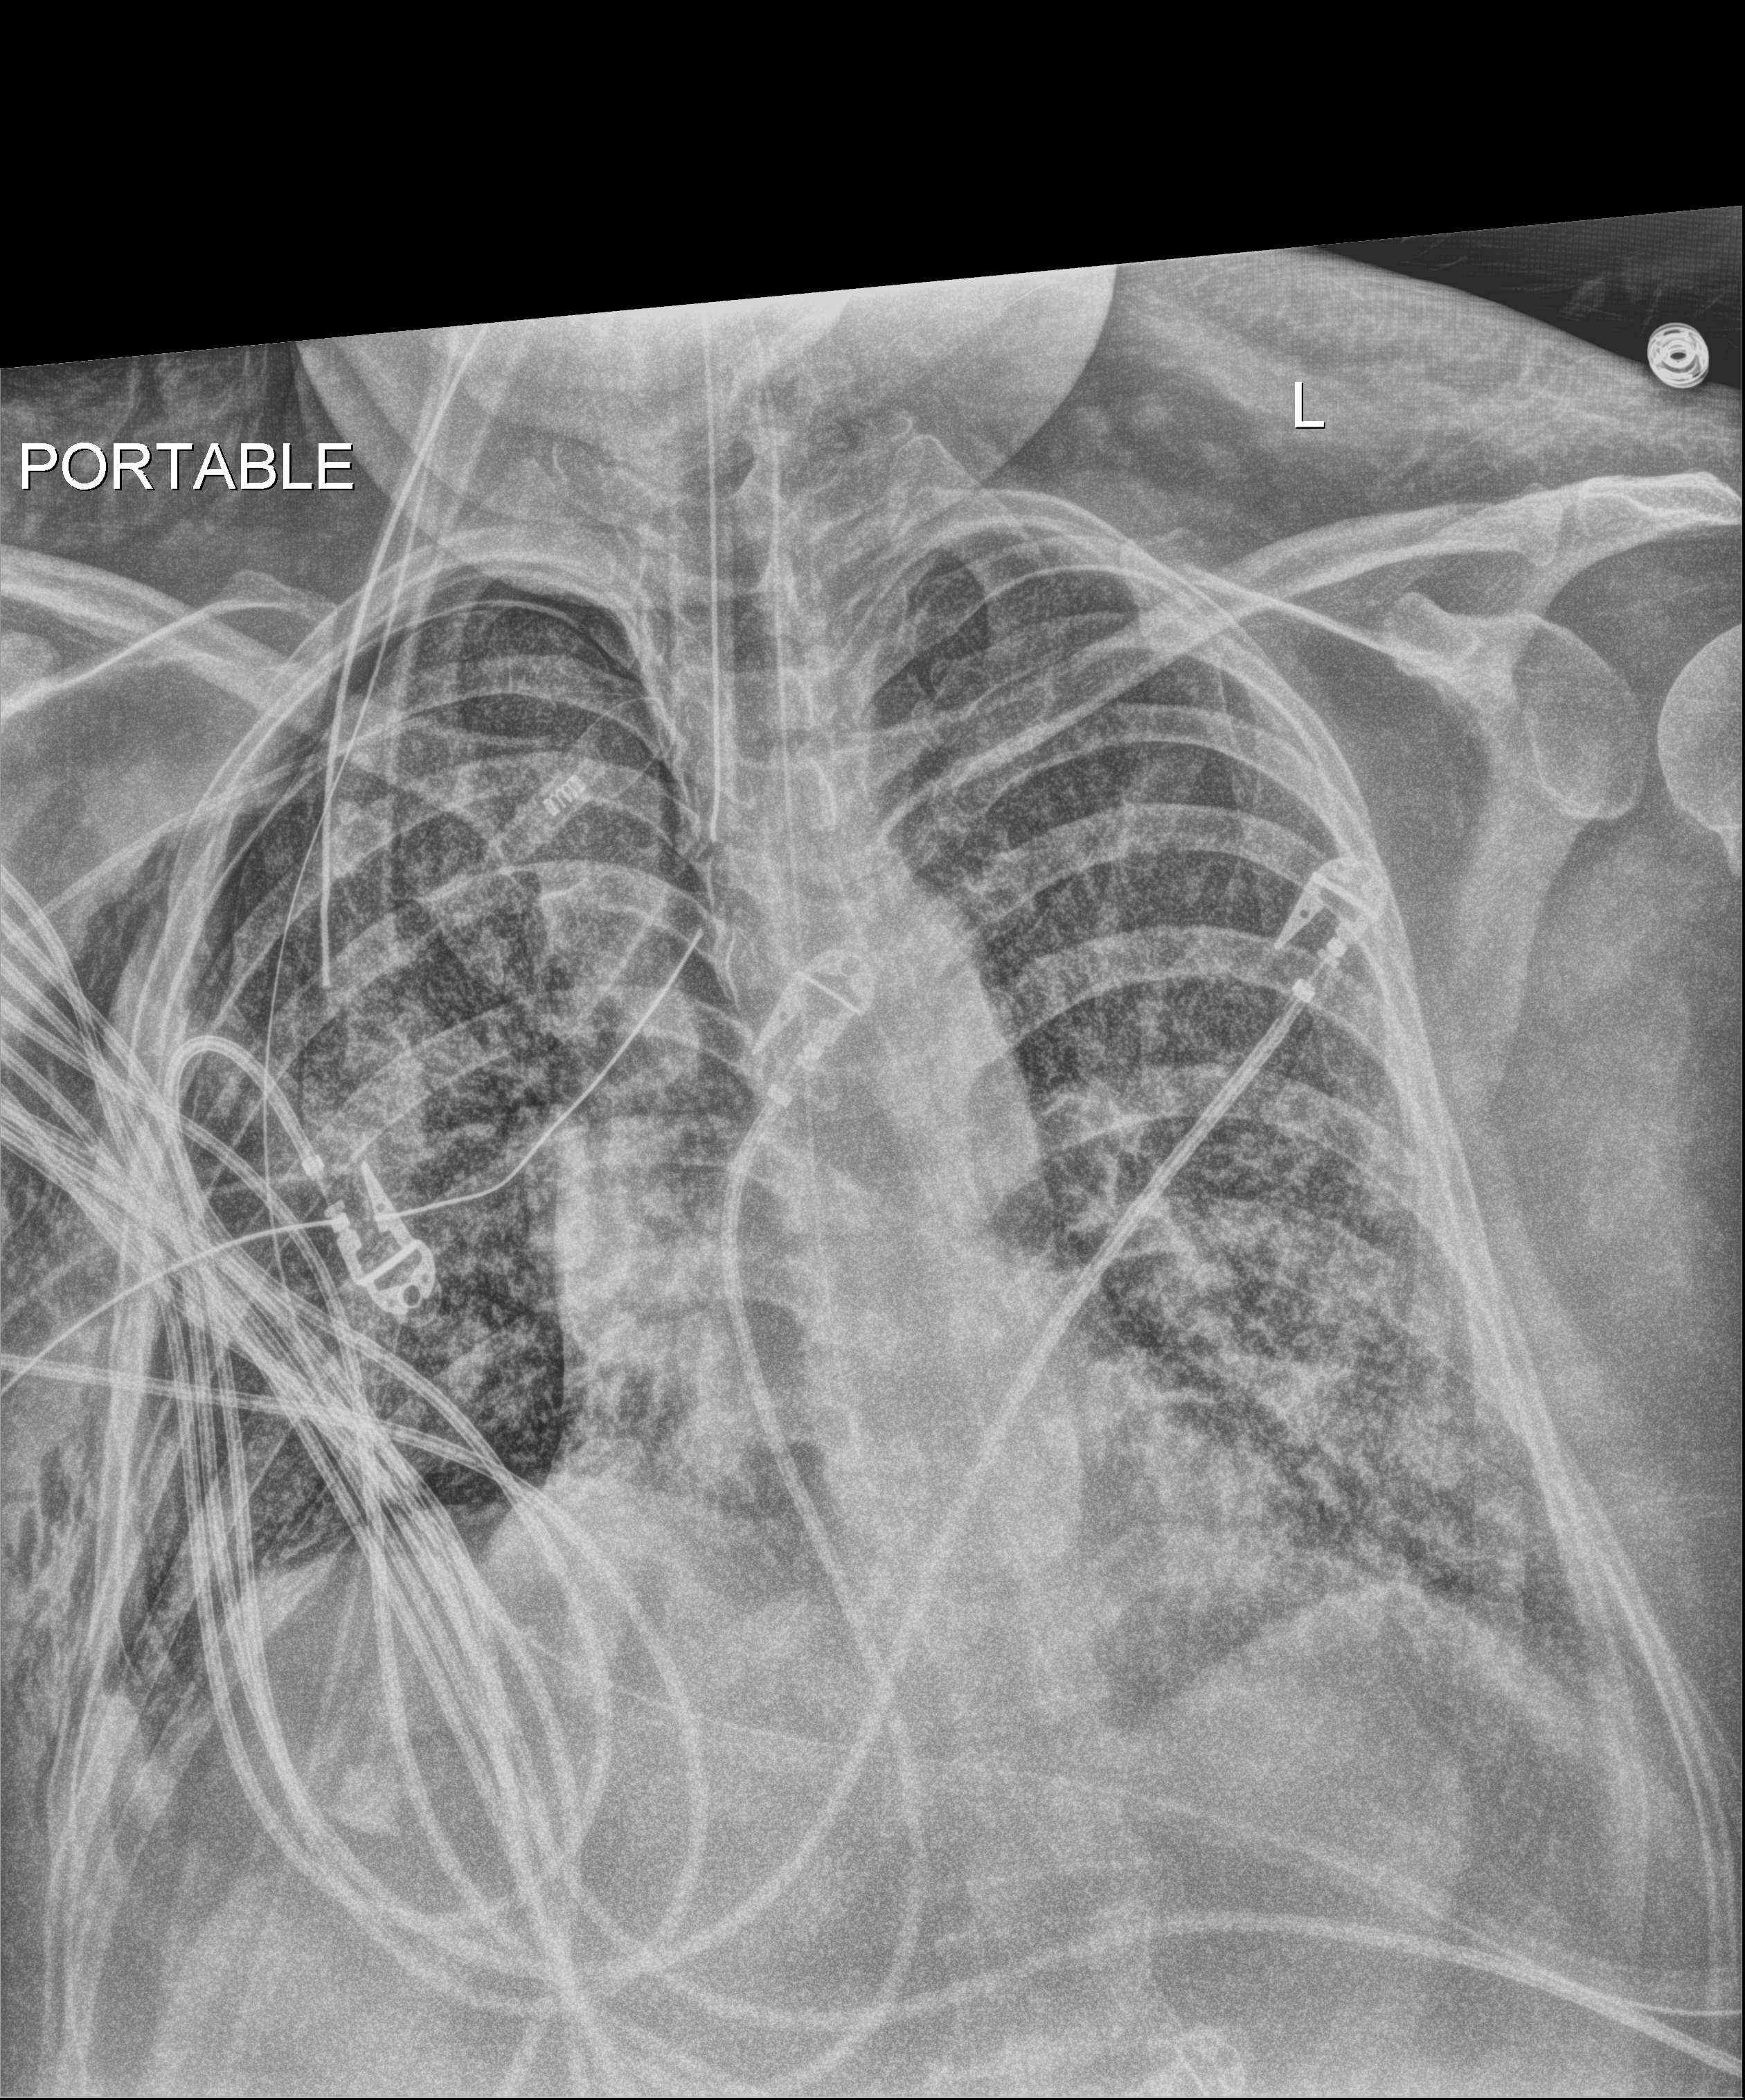
Portable chest radiograph, anteroposterior (AP) projection. Adult patient hospitalised with COVID-19, age 18–59 years.
From the hospital-stay record, not from the radiograph (when in the stay this image was taken is not recorded):
- smoking status (admission record): never
- admitted to intensive care during this hospital stay: yes
- mechanically ventilated during this hospital stay: yes